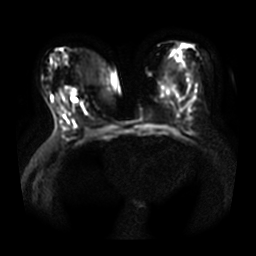
Breast MRI, one axial slice. Slice 15 of 33 in the series (ordered by position). Diffusion-weighted series; image 2 of 4 stored at this slice position (different b-values; order by instance number). 3 T. 256 × 256 image matrix, field of view 360 × 360 mm. Female patient.
Structures marked on this image (outlined manually by an expert reader):
- tumour on diffusion-weighted imaging: bounding box (x1, y1, x2, y2) in pixels: (67, 87, 76, 96)